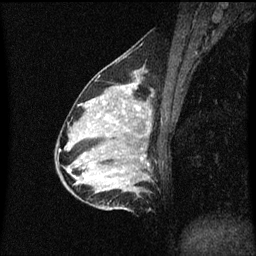
Breast MRI (dynamic contrast-enhanced), one sagittal slice. Slice 24 of 60 in the series (ordered by position). Dynamic contrast-enhanced series, image 2 of 3 at this slice position (ordered by acquisition). 1.5 T. TE 4.2 ms, TR 8.4 ms. 256 × 256 image matrix, field of view 200 × 200 mm. Female patient, age 34 years. Case-level facts recorded for this patient, not image findings: setting: breast cancer imaged before/during neoadjuvant chemotherapy; receptor status: HR-positive, HER2-negative.
Annotated regions visible in this slice (semi-automatically segmented with operator editing):
- analysis volume of interest (the breast-tissue region the enhancement analysis was run in; not a lesion): bounding box <69,70,153,209> (left, top, right, bottom; pixels)
- tumour enhancement mask (voxels above the 70 % enhancement threshold inside the analysis volume of interest): <128,86,140,111>